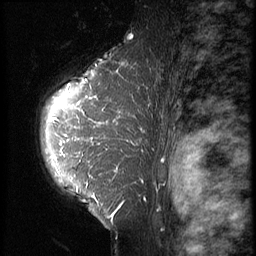
Breast MRI (dynamic contrast-enhanced), one sagittal slice. Position 46 of 64 along the scan axis. 3 images stored at this slice position (order not interpretable as contrast timing). 1.5 T. TE 4.2 ms, TR 9 ms. 256 × 256 image matrix, field of view 180 × 180 mm. Patient: female, 39 years. From the clinical record (not read from this slice): setting: breast cancer imaged before/during neoadjuvant chemotherapy; receptor status: HER2-positive.
Outlined on this slice (semi-automatically segmented with operator editing):
- analysis volume of interest (the breast-tissue region the enhancement analysis was run in; not a lesion): bounding box <31,47,150,239> (left, top, right, bottom; pixels)
- tumour enhancement mask (voxels above the 140 % enhancement threshold inside the analysis volume of interest): <53,63,145,217>